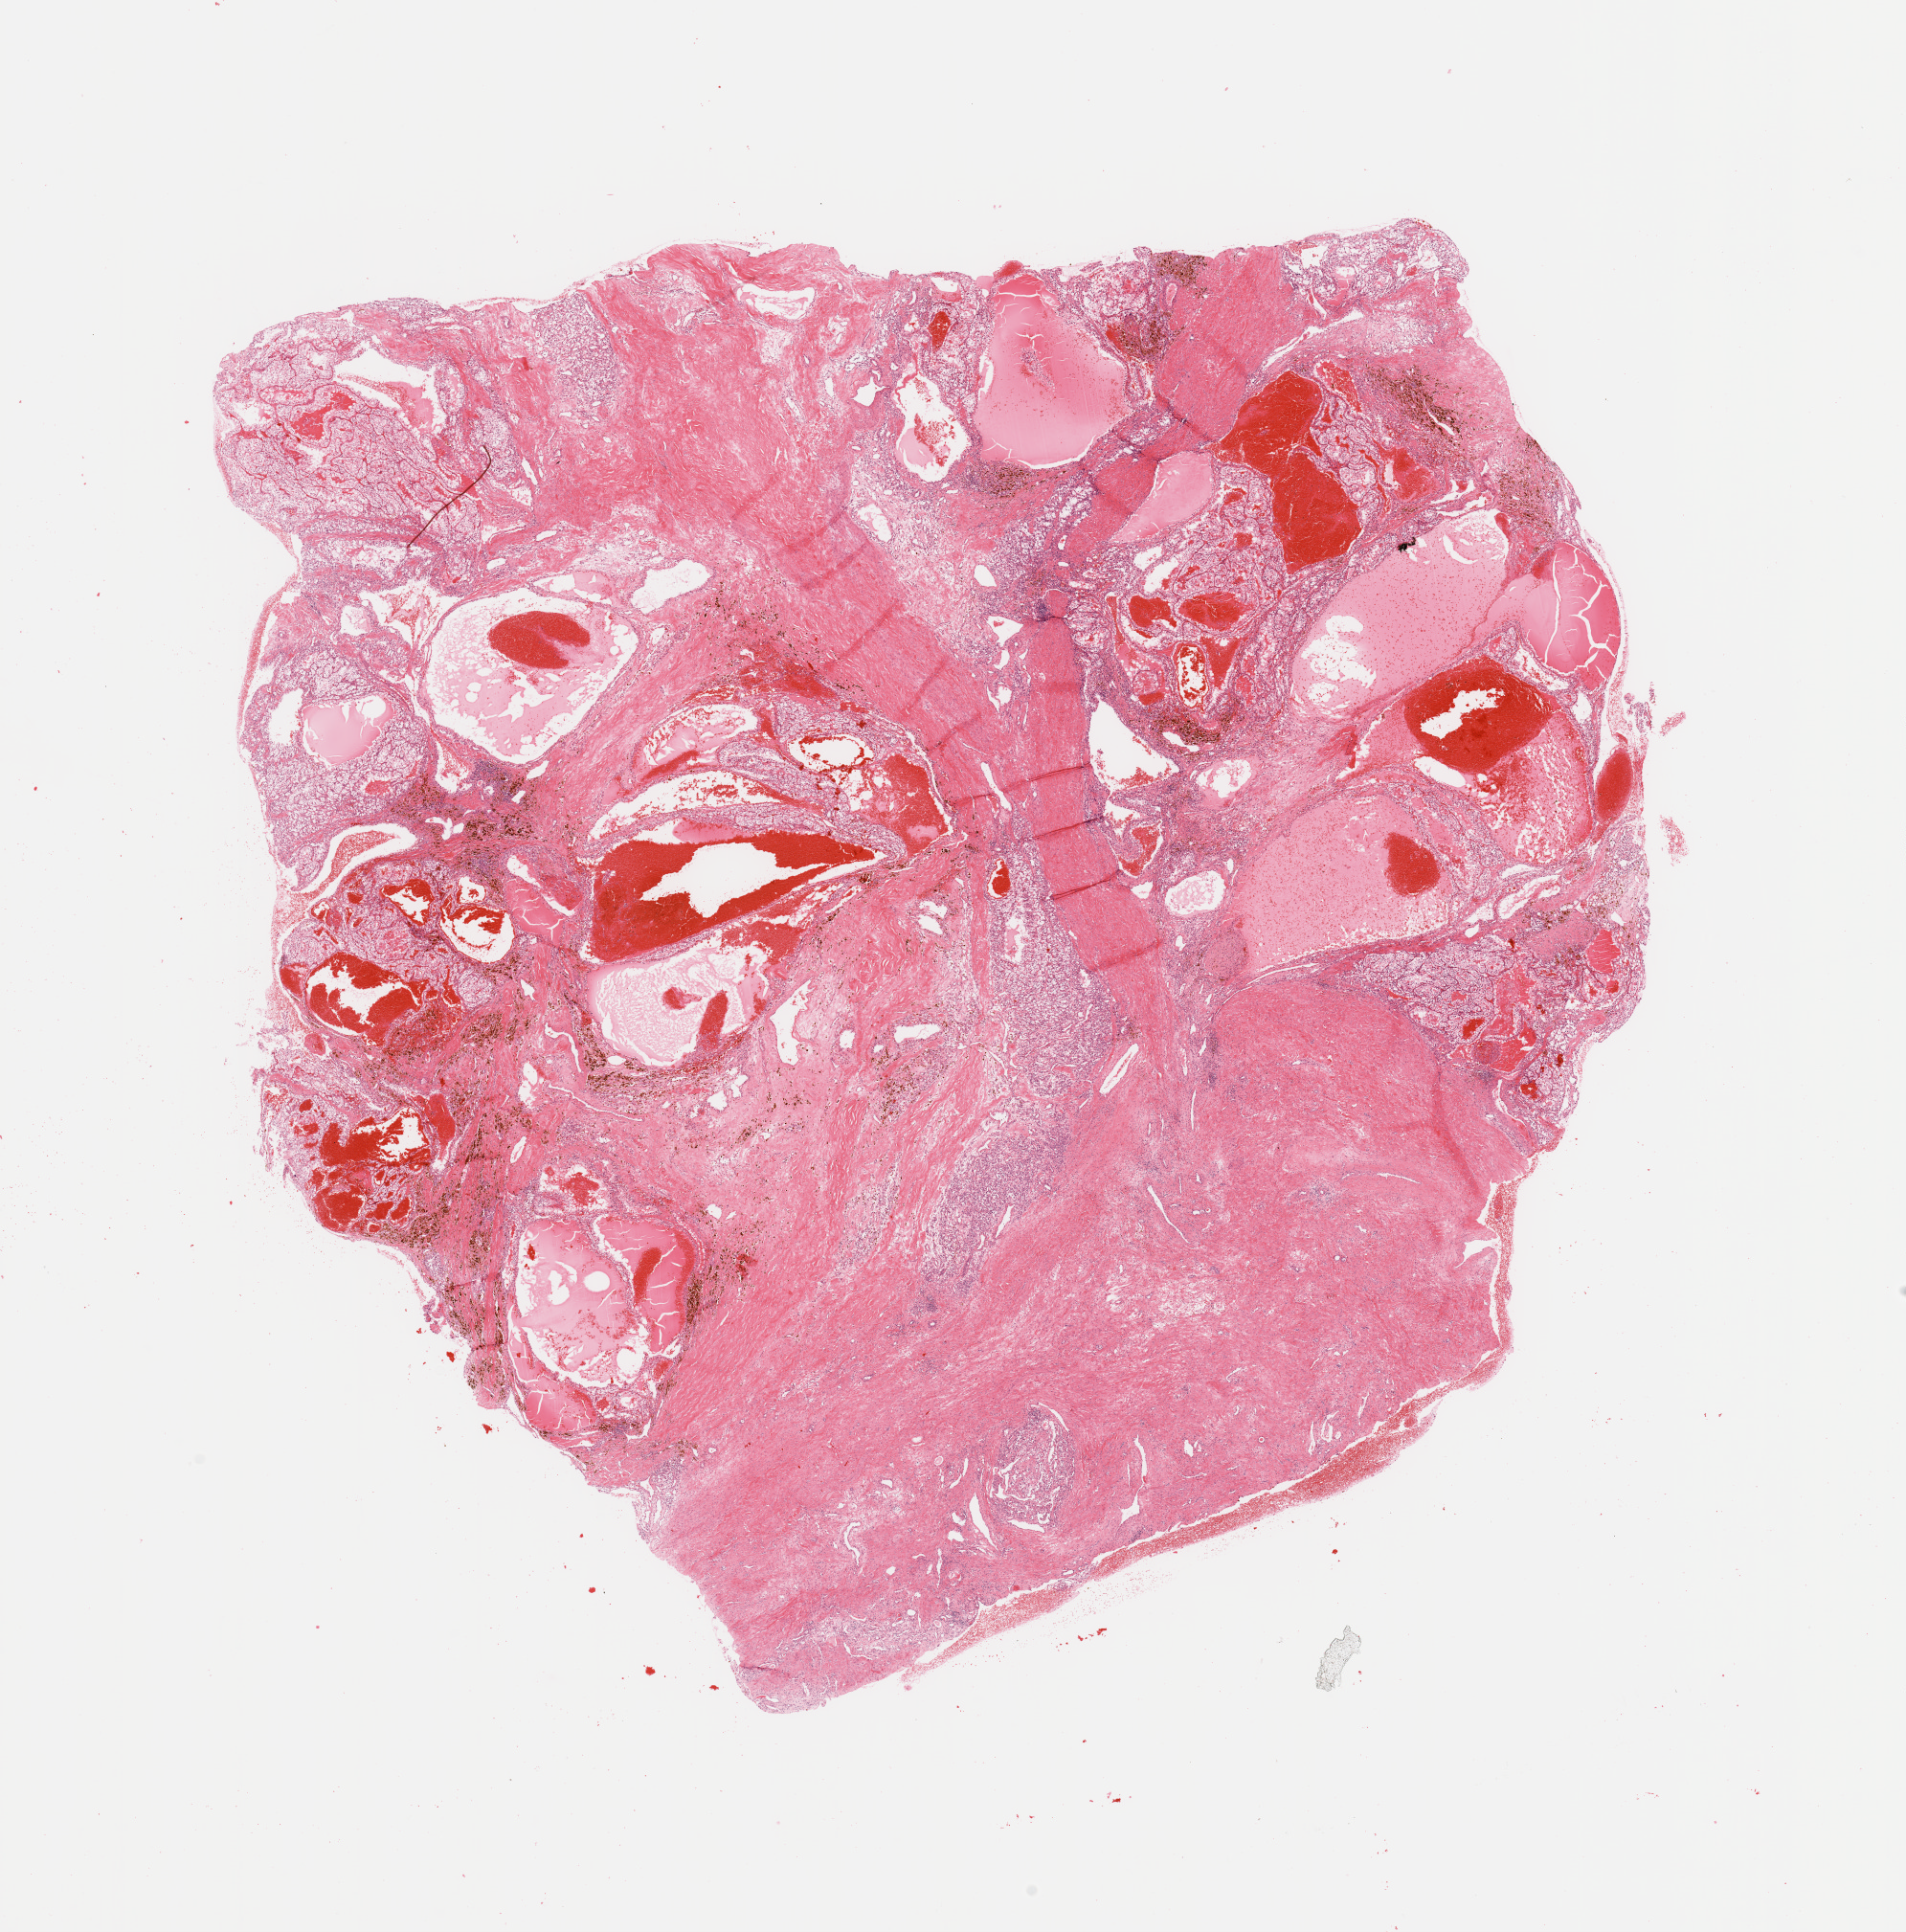
Whole-slide histology image, H&E — a low-resolution overview of the entire scanned area, about 15.8 x 16.0 mm (from a 20x scan); tumour tissue sample, sampled site: kidney. Female, 55 y/o. Composition of this section per pathologist review: tumour nuclei 60%, necrosis 5%.
Diagnosis: Renal cell carcinoma, NOS.